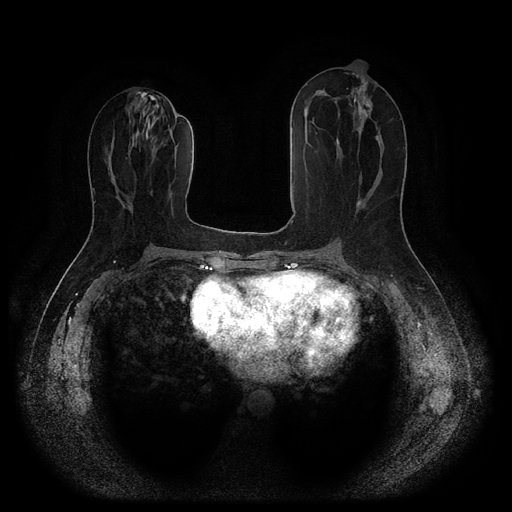
Breast MRI (dynamic contrast-enhanced, multi-phase), one axial slice. Slice 46 of 116 in the series (ordered by position). Dynamic contrast-enhanced series, time point 2 of 5 at this slice position (early post-contrast). 1.5 T. TE 2.6 ms, TR 5.3 ms. 512 × 512 image matrix. Female patient, age 53 years.
Annotated regions visible in this slice (semi-automatic segmentation, software-assisted and operator-edited):
- breast lesion (labelled 'tumour' in the annotation; benign lesions carry a separate 'benign' label): bounding box <358,102,371,115> (left, top, right, bottom; pixels)